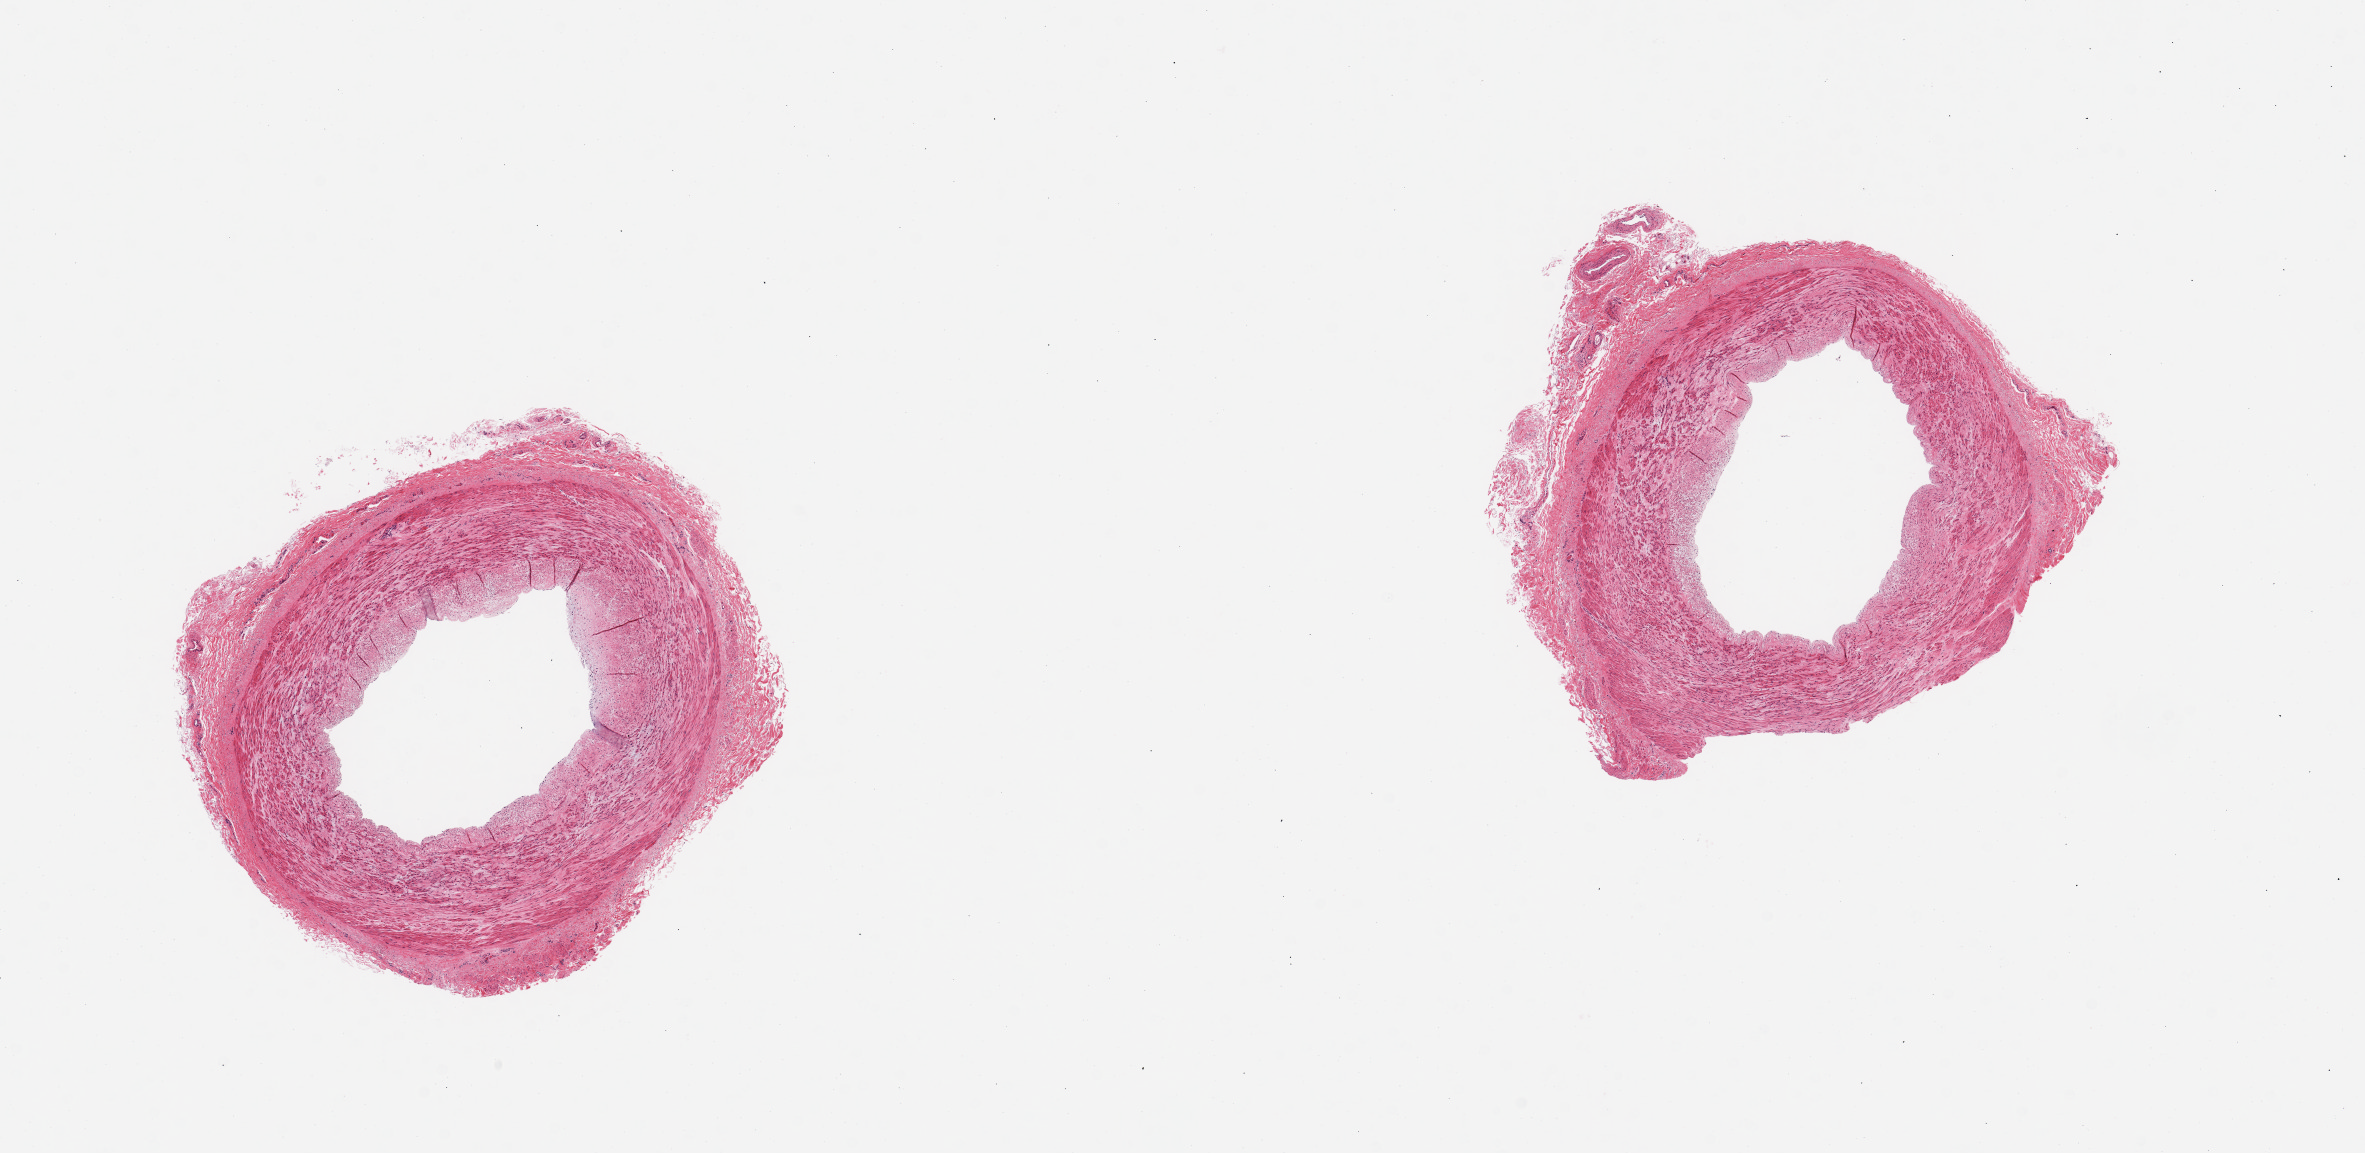
Whole-slide image, haematoxylin and eosin stain, low-resolution overview of the scanned area, about 18.7 x 9.1 mm (from a 20x scan). PAXgene-fixed, paraffin-embedded tissue. Target tissue: tibial artery. Donor tissue sample.
Review note (as recorded): 2 pieces; well trimmed; no plaques.